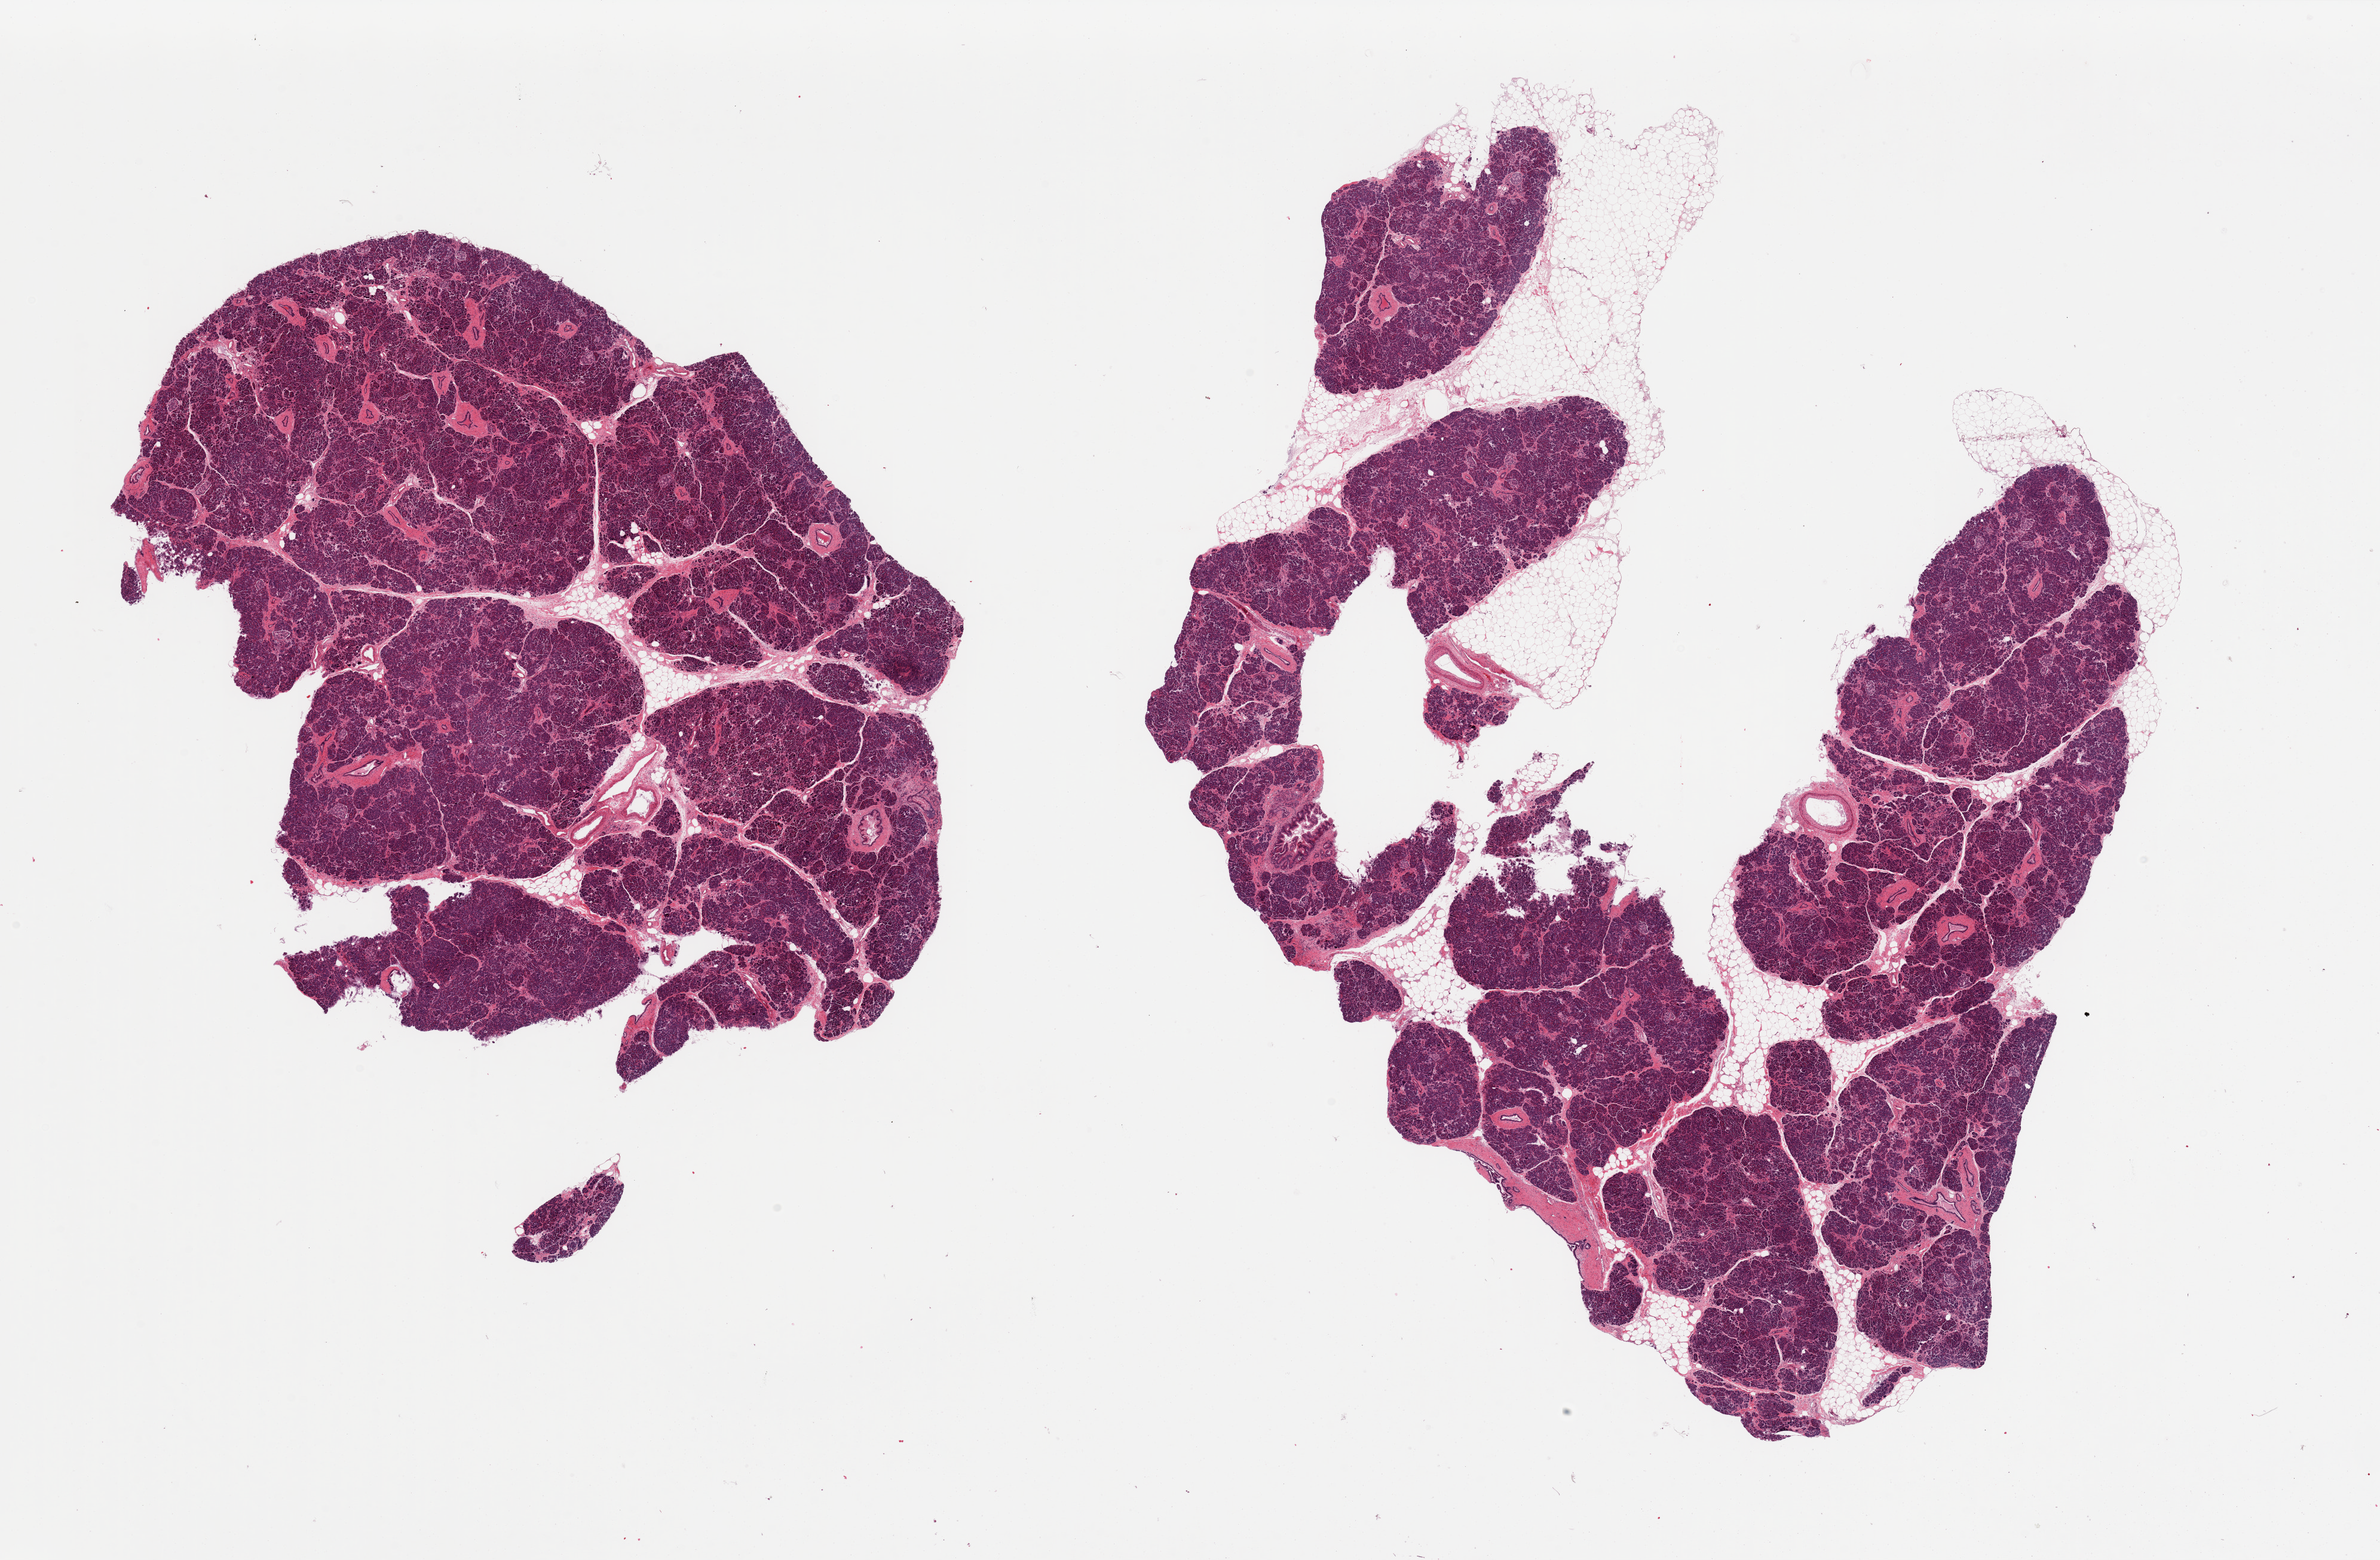
Digitized haematoxylin and eosin-stained section, brightfield — whole scanned area (about 31.5 x 20.7 mm) shown as a low-resolution overview; PAXgene-fixed paraffin-embedded (PFPE) section; section of pancreas (target tissue); donor tissue sample. Male donor.
- review note (as recorded): 2 pieces: 1 has 20% fat; other well trimmed